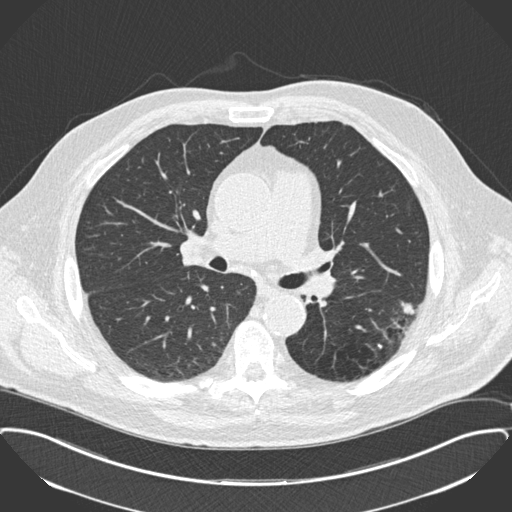
Low-dose screening chest CT, one axial slice; slice 102 of 175 in the series (ordered by position); lung window (W 1500 / L -600 HU); 2 mm slice thickness; 512 × 512 image matrix, field of view 400 × 400 mm.
Annotated regions visible in this slice (manually delineated by an expert):
- lesion 1 (tumor, lower lobe of left lung): bounding box (x1, y1, x2, y2) in pixels: (401, 302, 415, 315)